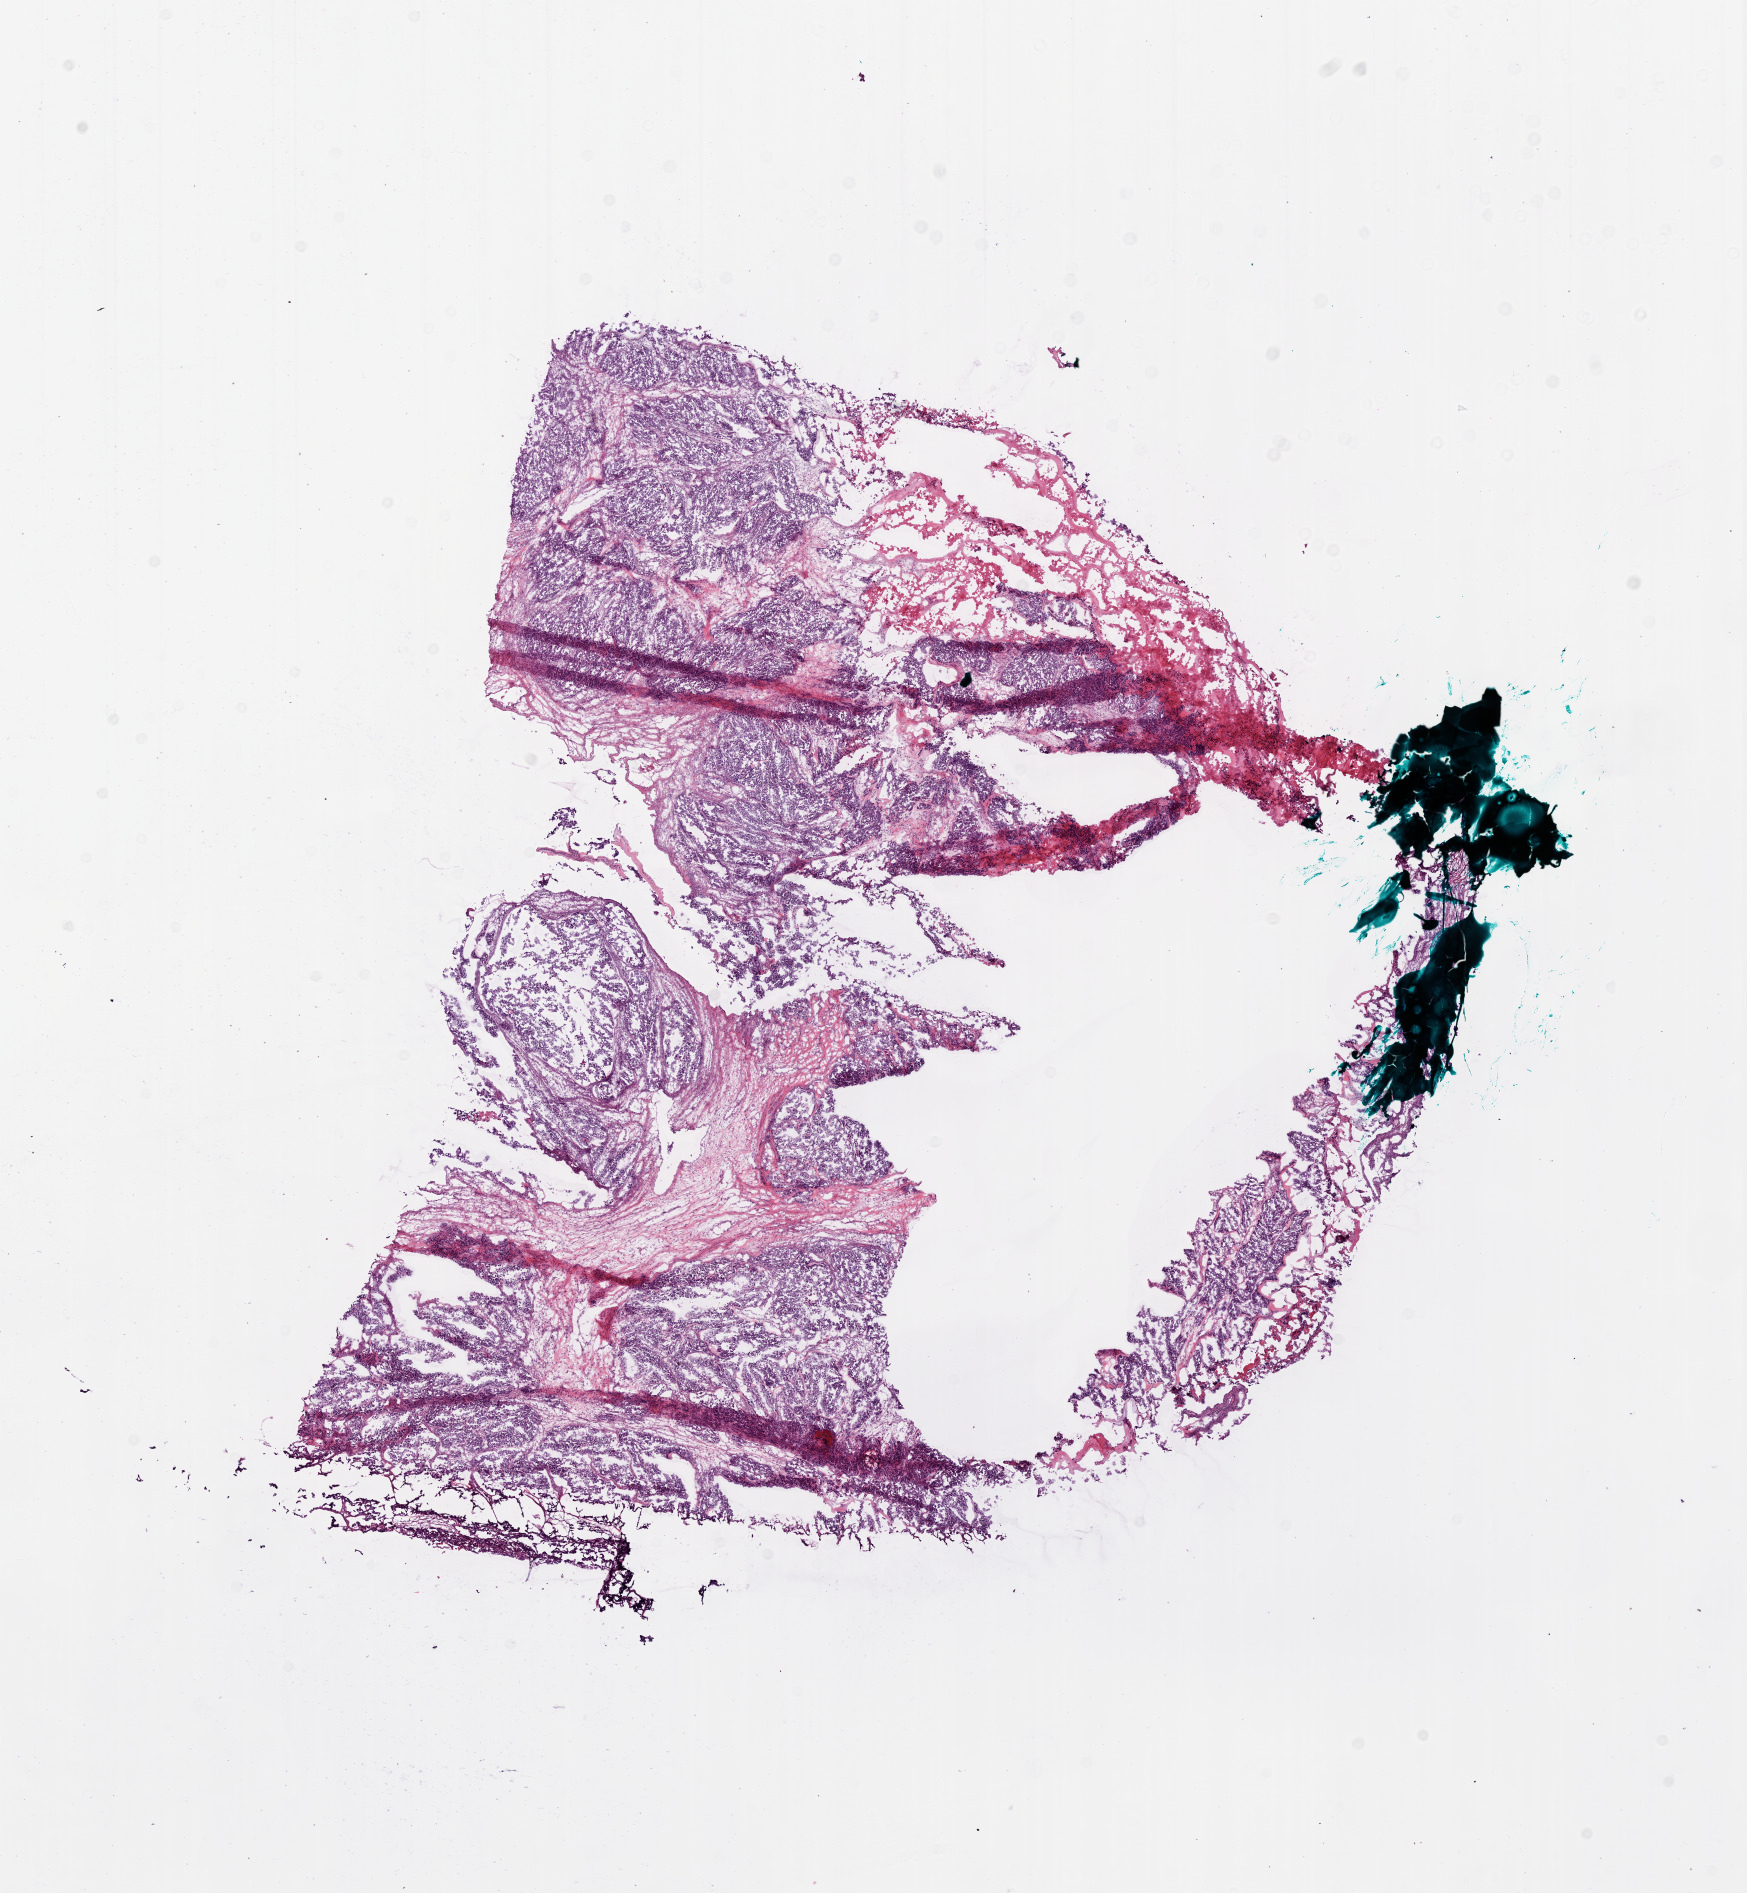
Hematoxylin and eosin (H&E) stained whole-slide image — a low-resolution overview of the entire scanned area, about 14.0 x 15.2 mm (acquisition: 20x scan); frozen section; sample: primary tumour, ovary. Female, age 78 years at initial diagnosis.
Pathologic diagnosis: Serous cystadenocarcinoma, NOS.